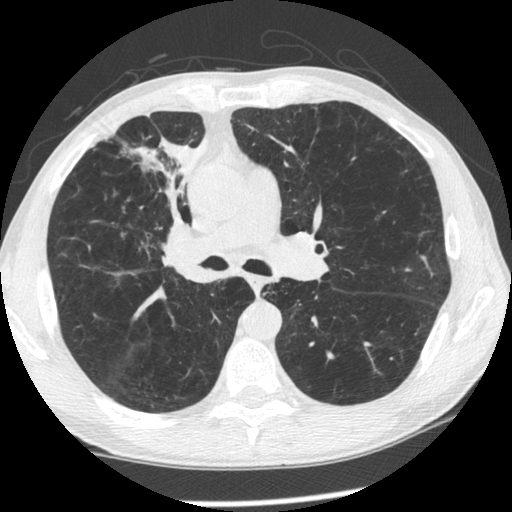
Low-dose screening chest CT, one axial slice. Slice 141 of 261 in the series (ordered by position). Reconstruction kernel STANDARD. Lung window (W 1500 / L -600 HU). 1.25 mm slice thickness. 512 × 512 image matrix, field of view 340 × 340 mm.
Outlined on this slice (manually delineated by an expert):
- lesion 1 (tumor, upper lobe of right lung): box from (x=132, y=136) to (x=208, y=236) px